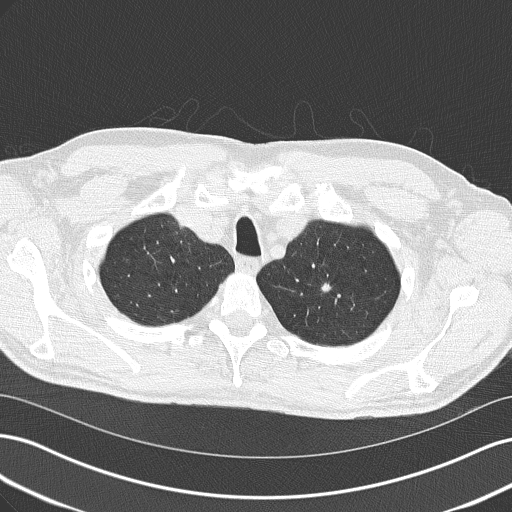
Low-dose screening chest CT, axial slice, second screening round (one year after baseline), lung window (W 1500 / L -600 HU), 2 mm slice thickness, slice 38 of 185 in the series. Male, age 64 years at enrolment. Former smoker at enrolment.
• Expert reader's lesion annotation, box from (x=303, y=270) to (x=338, y=308) px.
• The screening reader recorded 2 non-calcified nodules or masses ≥4 mm on this exam (left upper lobe, left upper lobe); which of them this box marks is not recorded.
• Participant outcome: lung cancer diagnosed 482 days after this screen (after the third annual screen) — adenocarcinoma, NOS, left upper lobe, poorly differentiated (G3), stage IA (AJCC 6th edition), 10 mm at pathology.